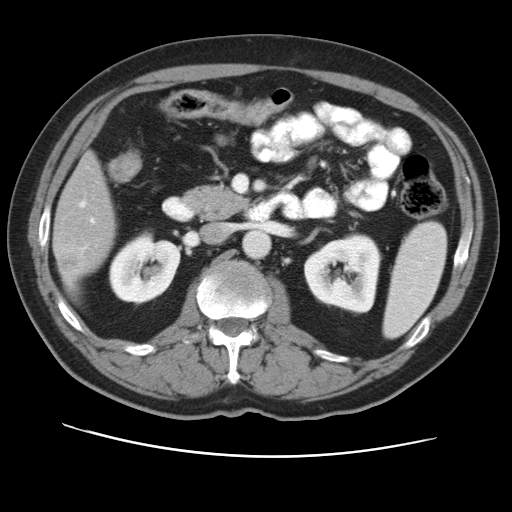
Contrast-enhanced abdominal CT, one axial slice. Position 19 of 49 along the scan axis. Reconstruction kernel STANDARD. 120 kVp. Intravenous contrast given. Soft-tissue window (W 400 / L 40 HU). 512 × 512 image matrix, field of view 374 × 374 mm. Male patient, age 59 years. From the clinical record (not read from this slice): diagnosis: colorectal cancer liver metastases, imaged before liver resection; multiple liver metastases: yes; largest metastasis: 6.3 cm; chemotherapy before resection: yes.
Structures marked on this image (outlined manually by an expert reader):
- hepatic veins: bounding box <81,202,85,206> (left, top, right, bottom; pixels)
- liver: <55,156,116,289>
- planned liver remnant (the part of the liver to remain after resection): <61,156,116,238>
- portal vein (with intrahepatic branches): <82,218,94,250>
- liver metastasis: <60,257,81,274>